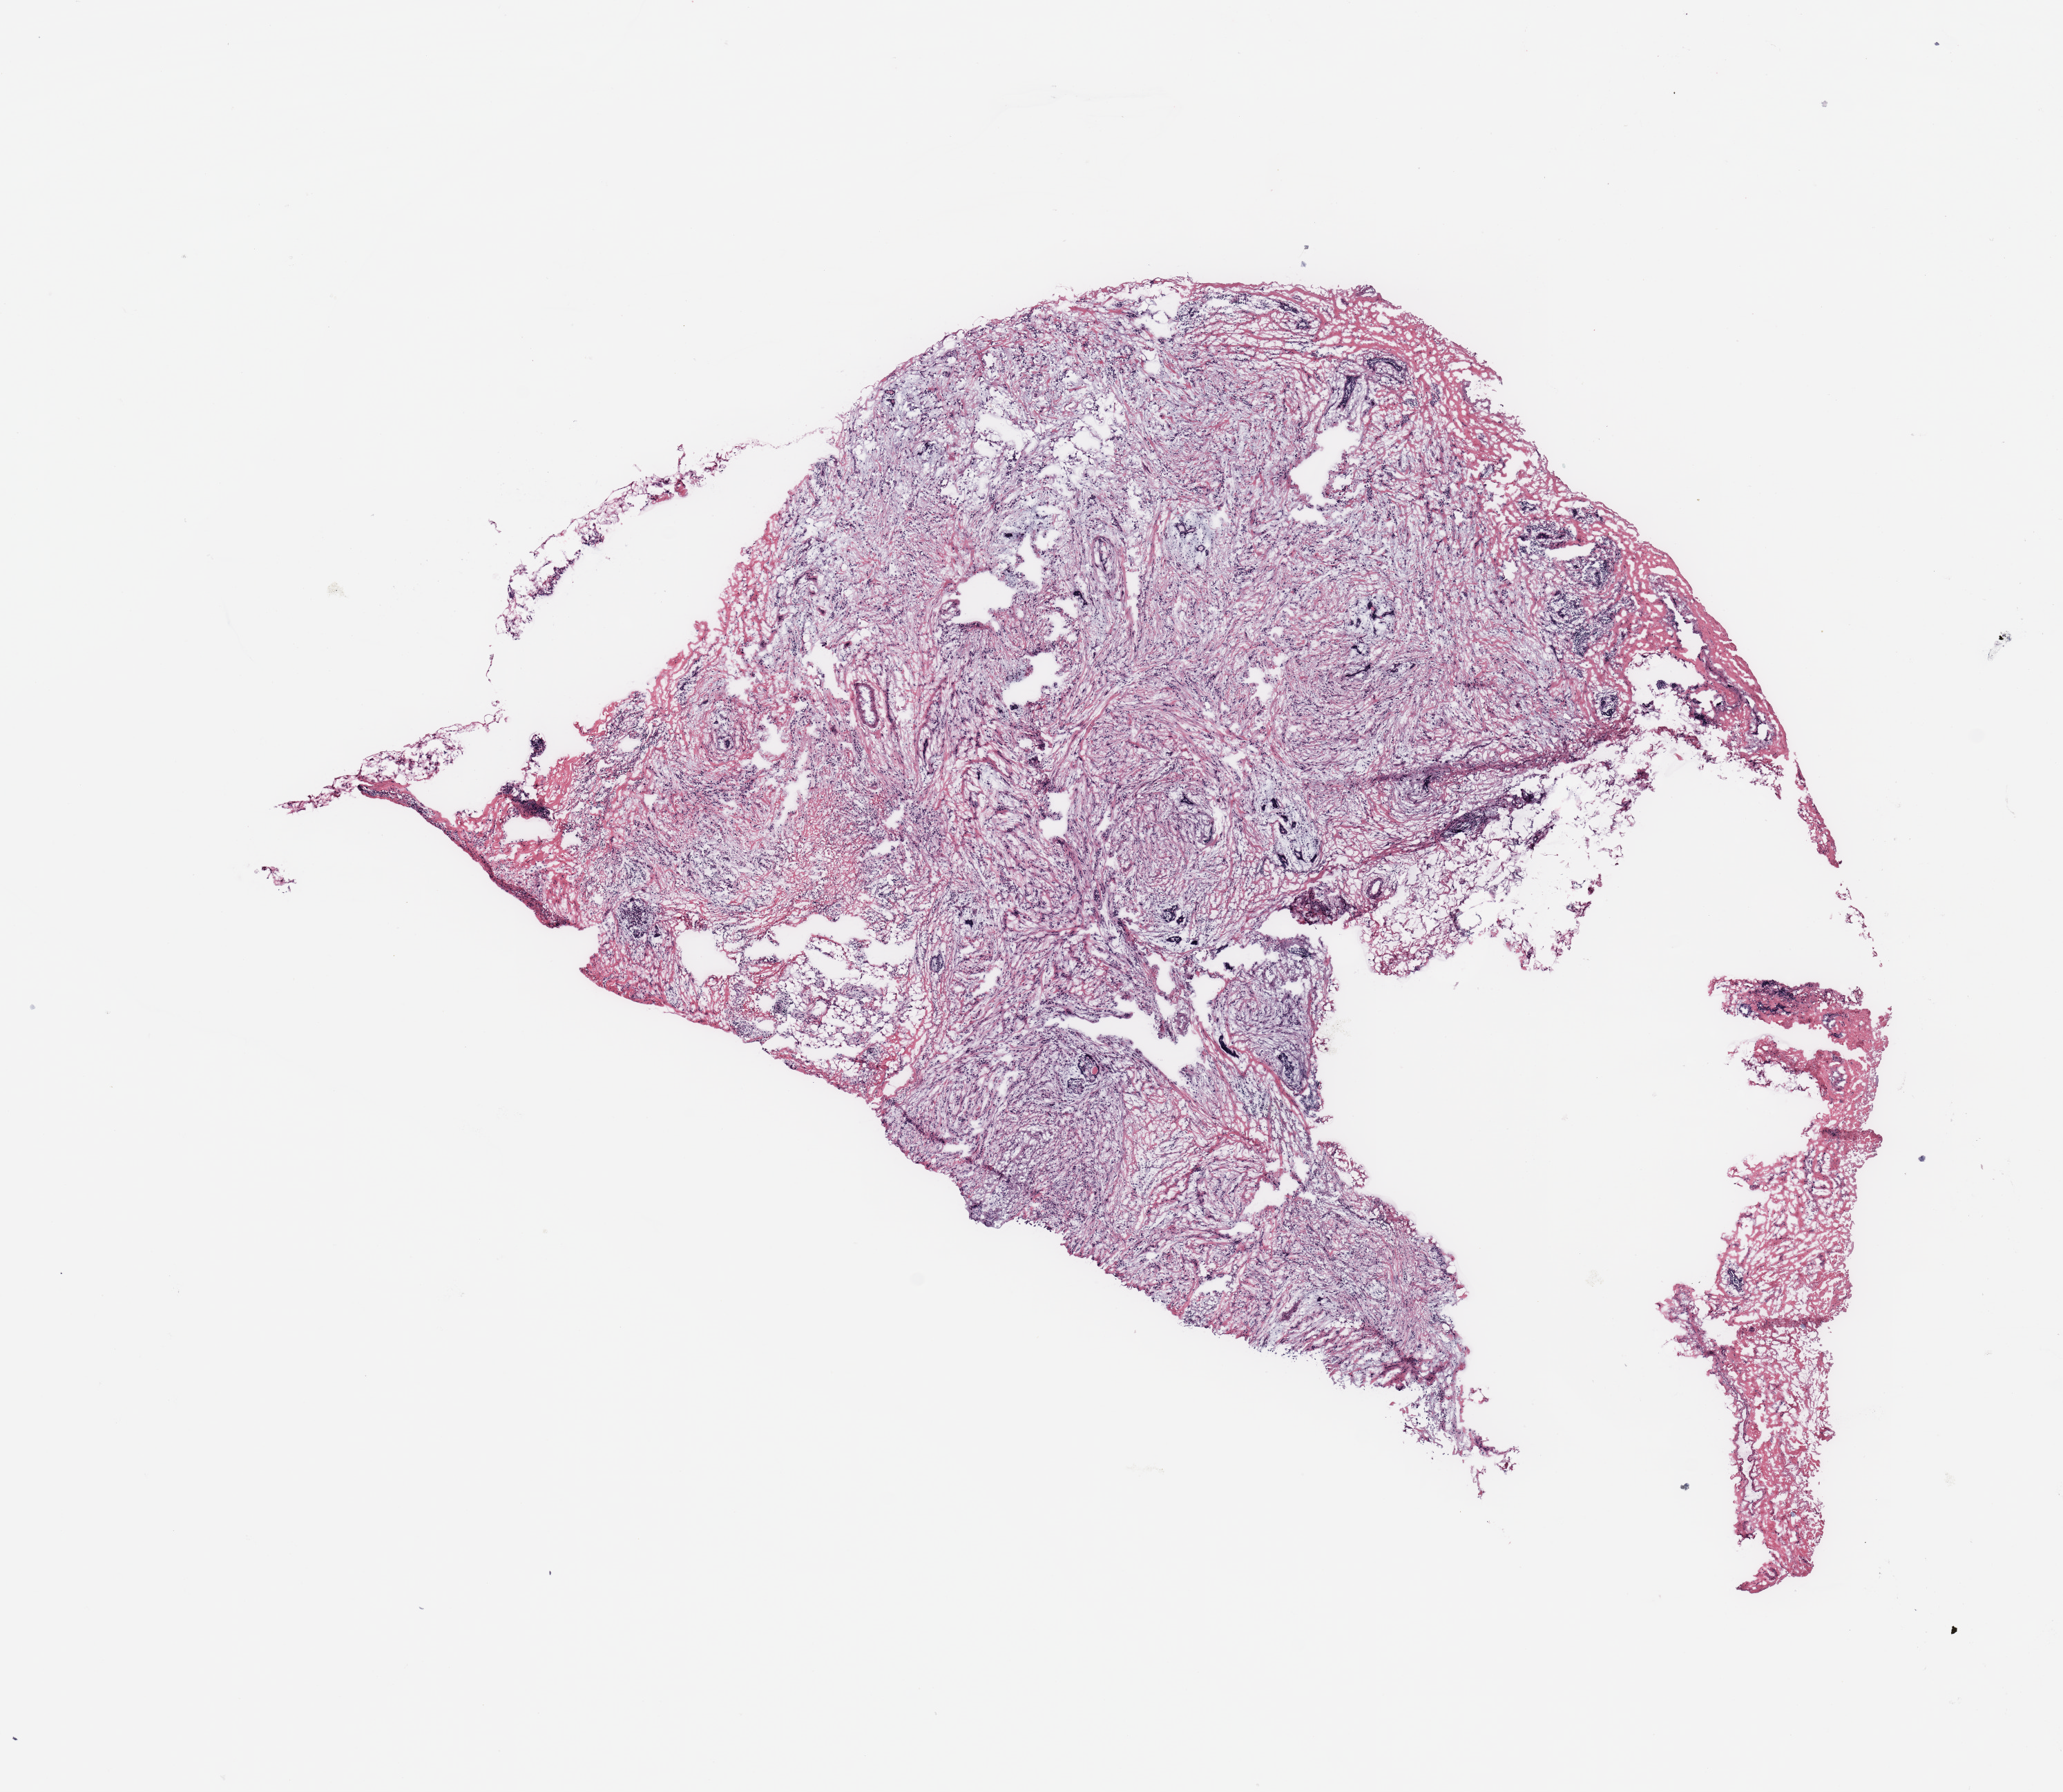
Hematoxylin and eosin (H&E) stained whole-slide image — a low-resolution overview of the entire scanned area, about 11.8 x 10.3 mm, breast, tissue type not recorded.
* patient diagnosis (cohort enrolment): breast cancer (breast)